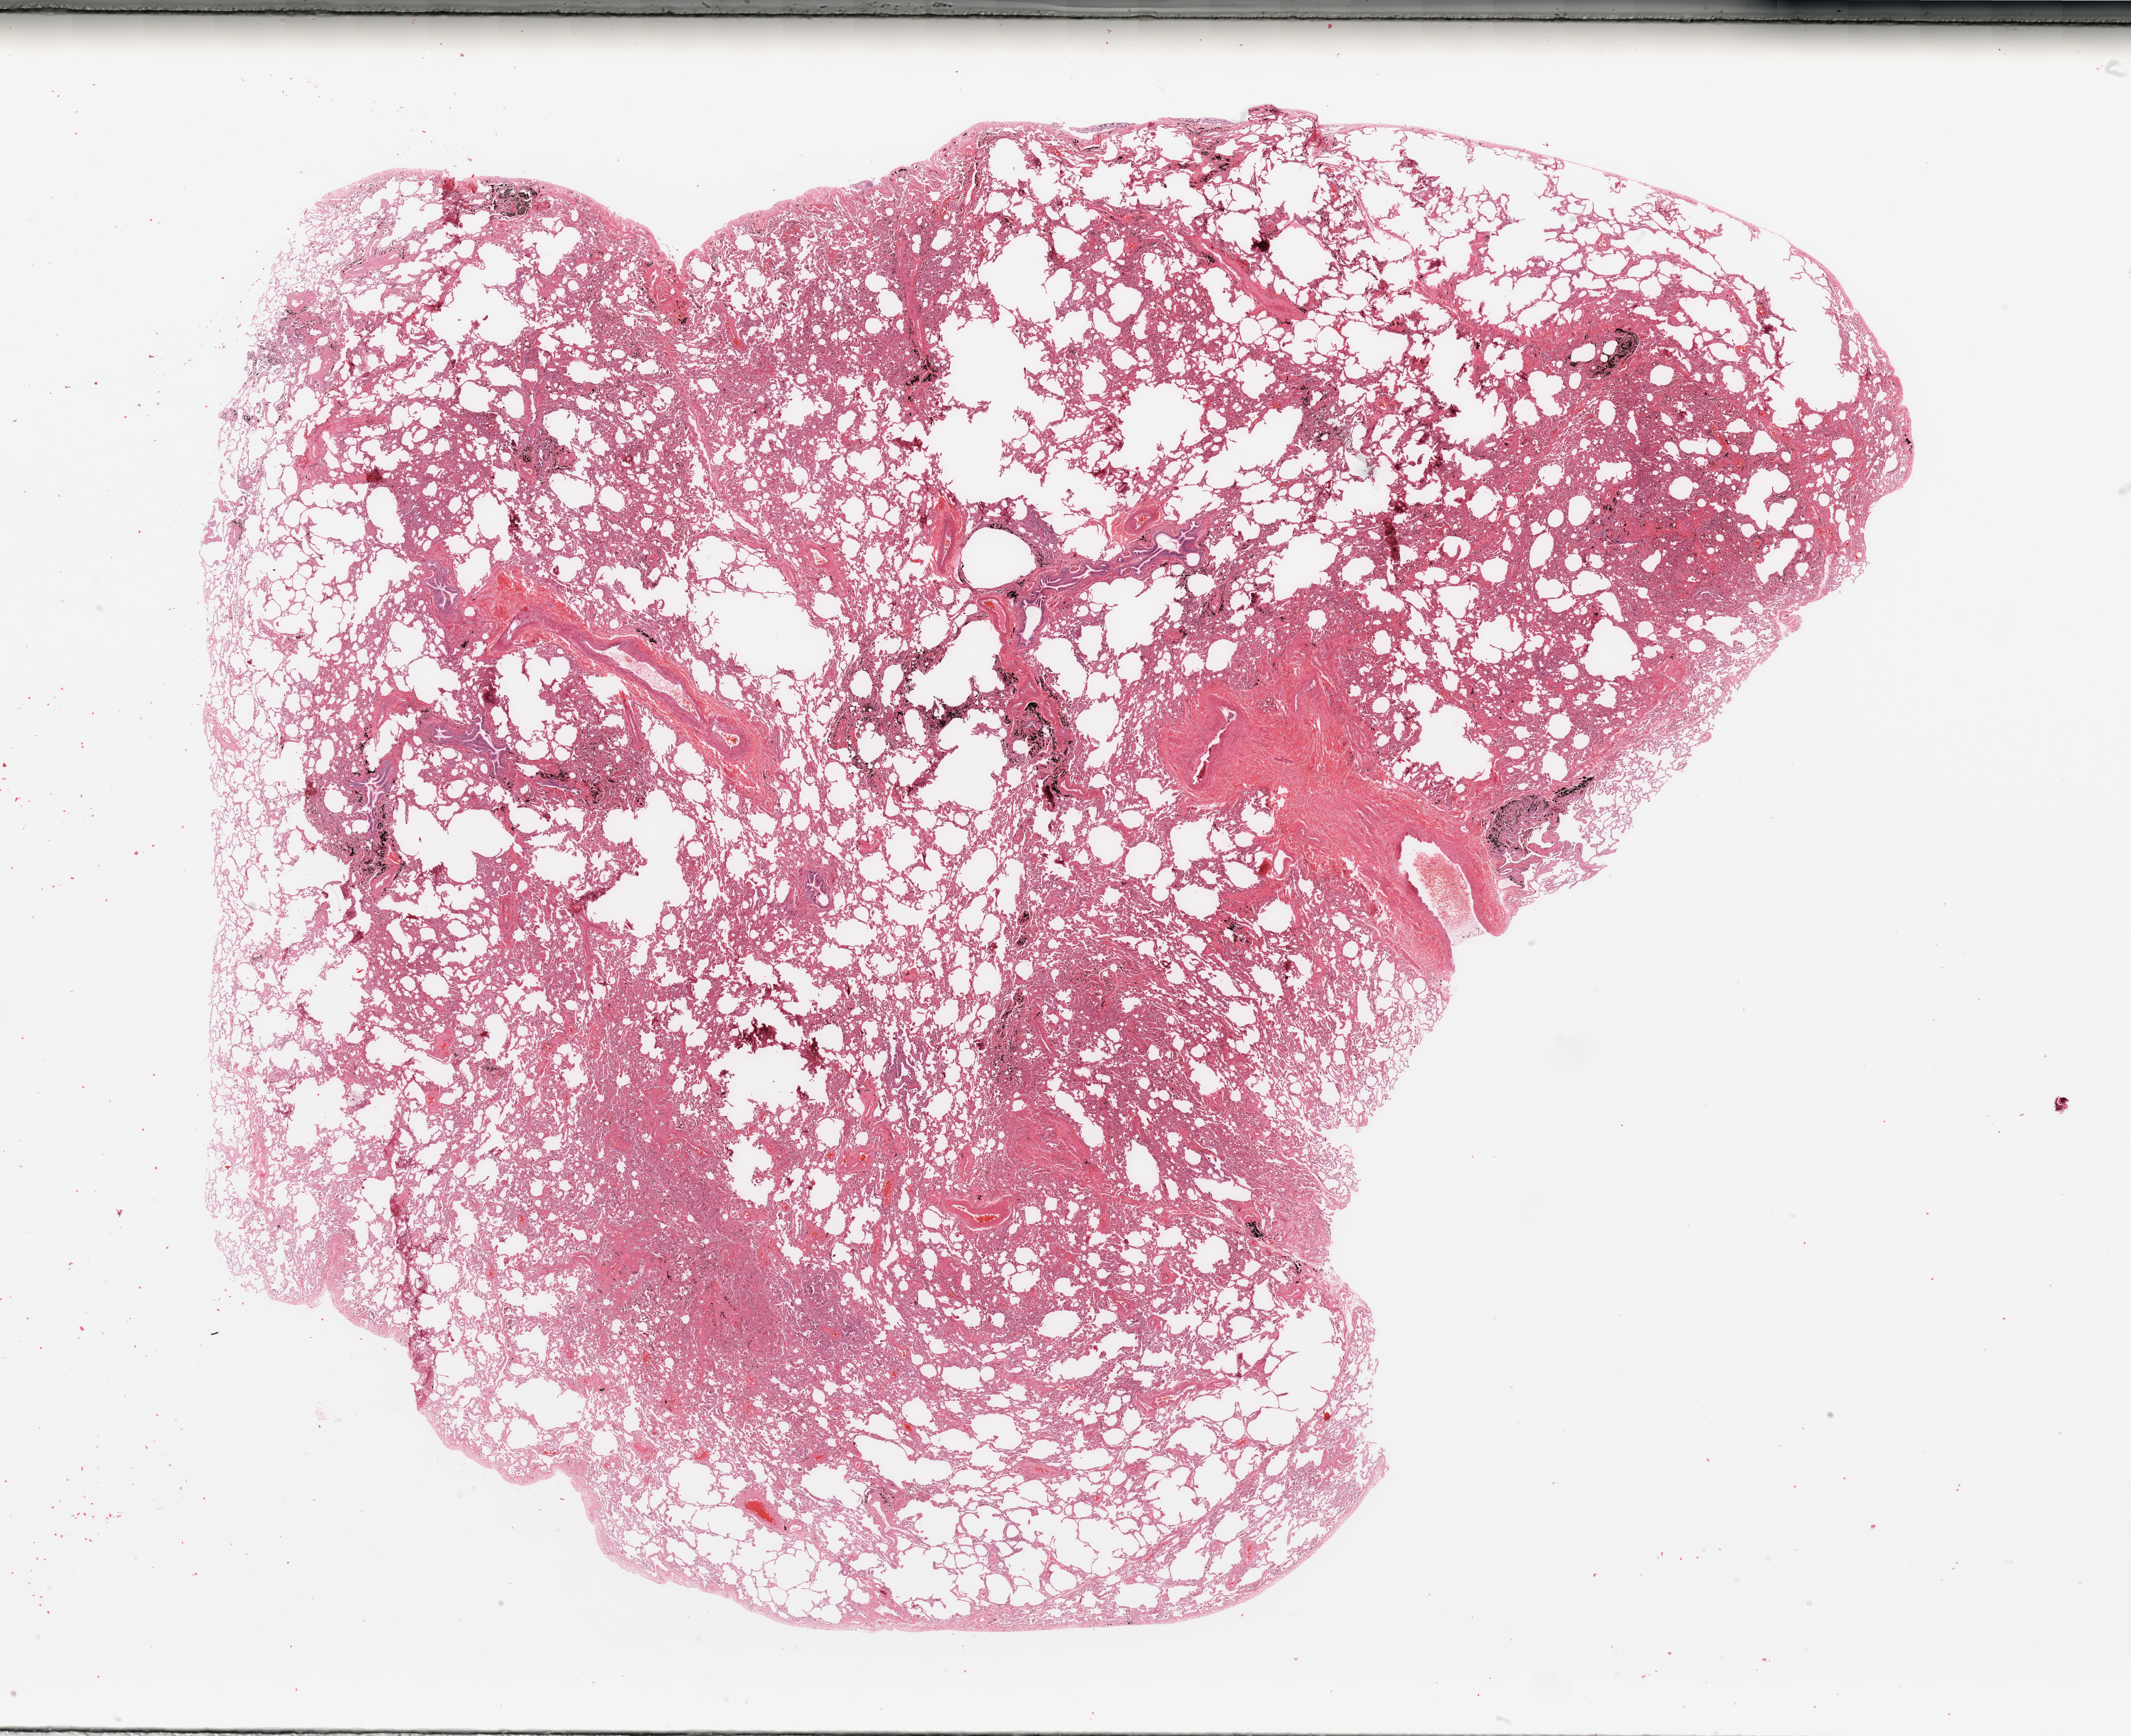
Digitized H&E tissue section (whole slide) — a low-resolution overview of the entire scanned area, about 29.5 x 24.1 mm, lung, normal (non-tumour) tissue. Patient: male, age 55 years.
This section: normal (non-tumour) tissue from the same patient. Patient diagnosis: Adenocarcinoma, NOS.